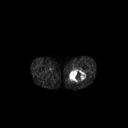
FDG PET of an extremity soft-tissue mass (from a PET/CT study), one axial slice; position 250 of 267 along the scan axis; 3.27 mm slice thickness; 128 × 128 image matrix. Male patient, age 44 years. From the clinical record (not read from this slice): histological type: undifferentiated pleomorphic liposarcoma; grade: high; site of the primary tumour: left thigh.
Outlined on this slice (expert contour drawn on MRI and transferred to this co-registered scan by the dataset authors):
- gross tumour volume including surrounding oedema: bounding box (x1, y1, x2, y2) in pixels: (68, 69, 86, 83)
- gross tumour volume (mass): (70, 69, 85, 81)